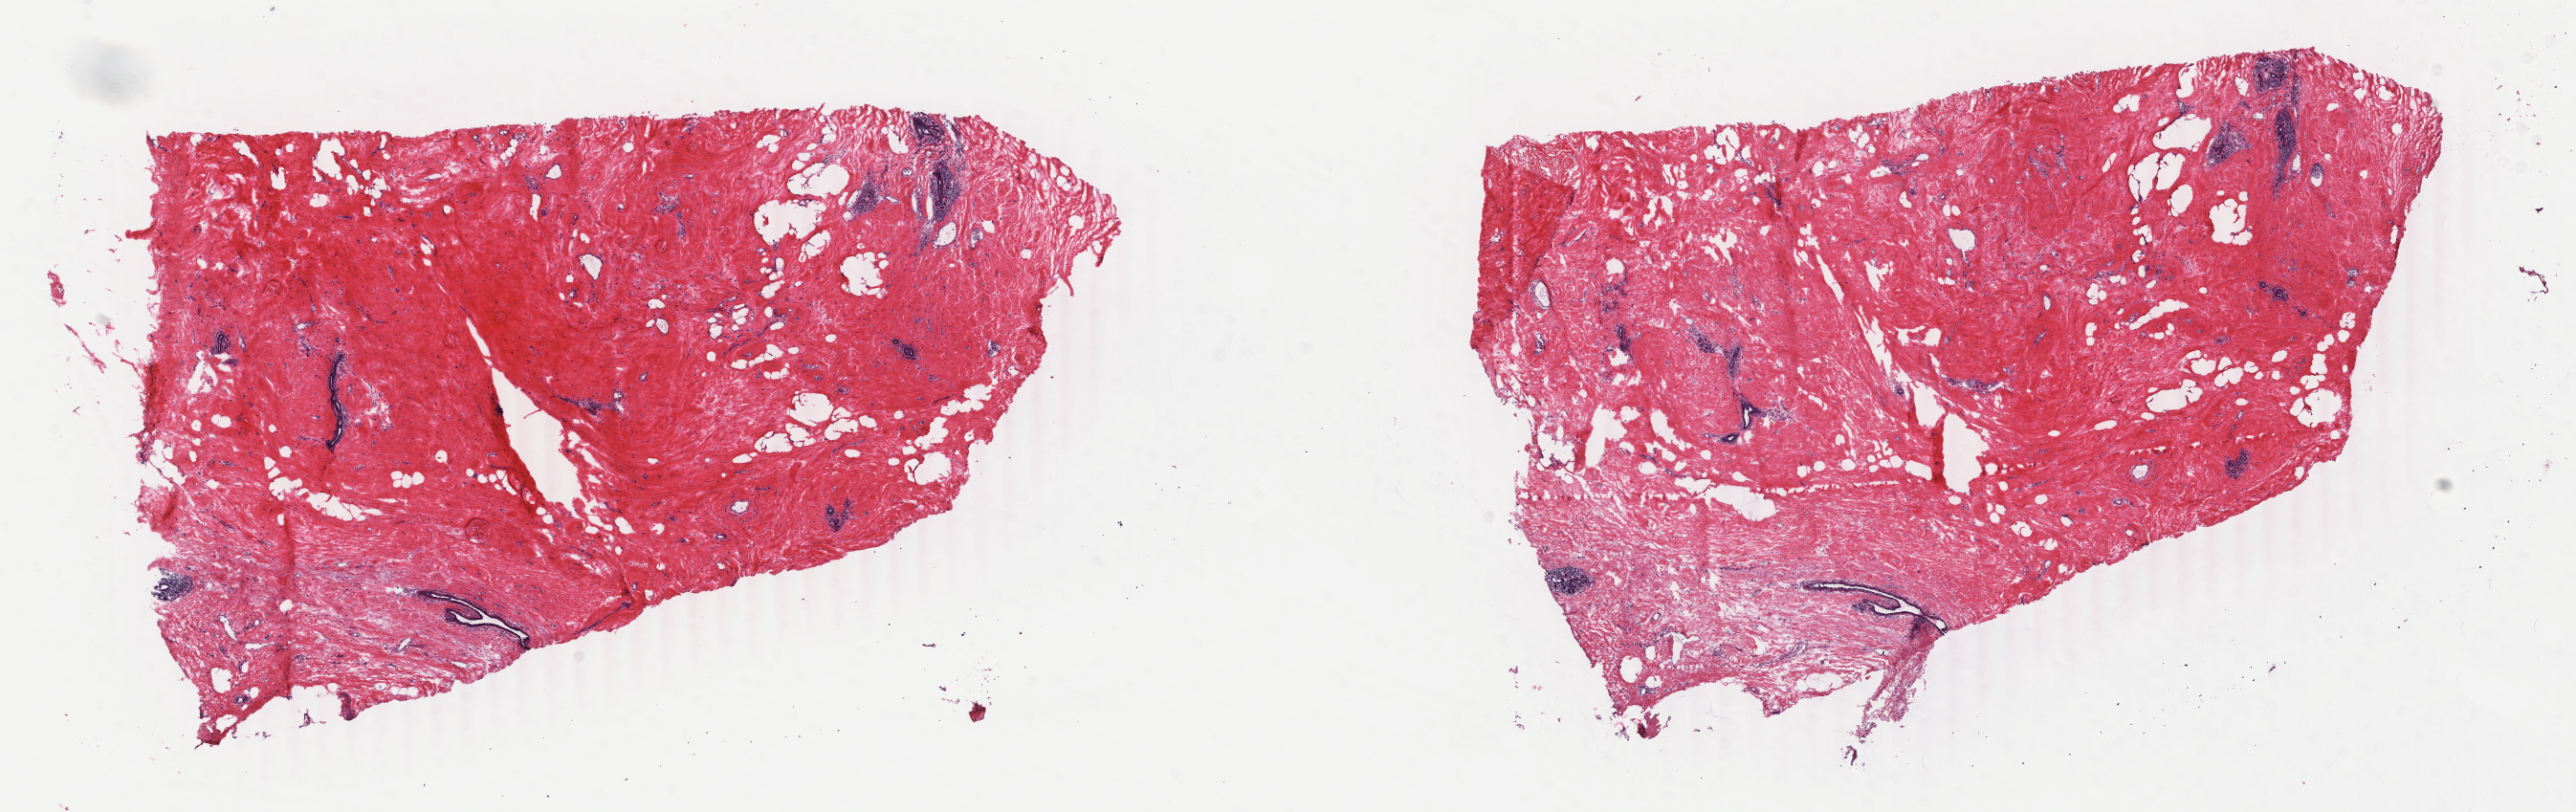
Hematoxylin and eosin (H&E) stained whole-slide image — shown as a low-resolution overview of the whole scanned area (about 21.4 x 6.8 mm); frozen section; sample: primary tumour, breast. Female, age 54 years at initial diagnosis. Composition of this section per pathologist review: tumour cells 0%, tumour nuclei 0%, normal cells 10%, stromal cells 90%, necrosis 0%. Infiltration values recorded for this section: lymphocyte infiltration 3%, monocyte infiltration 0%, neutrophil infiltration 0%.
* diagnosis: Infiltrating duct carcinoma, NOS
* AJCC pathologic stage: IIA
* TNM: T2 N0 M0